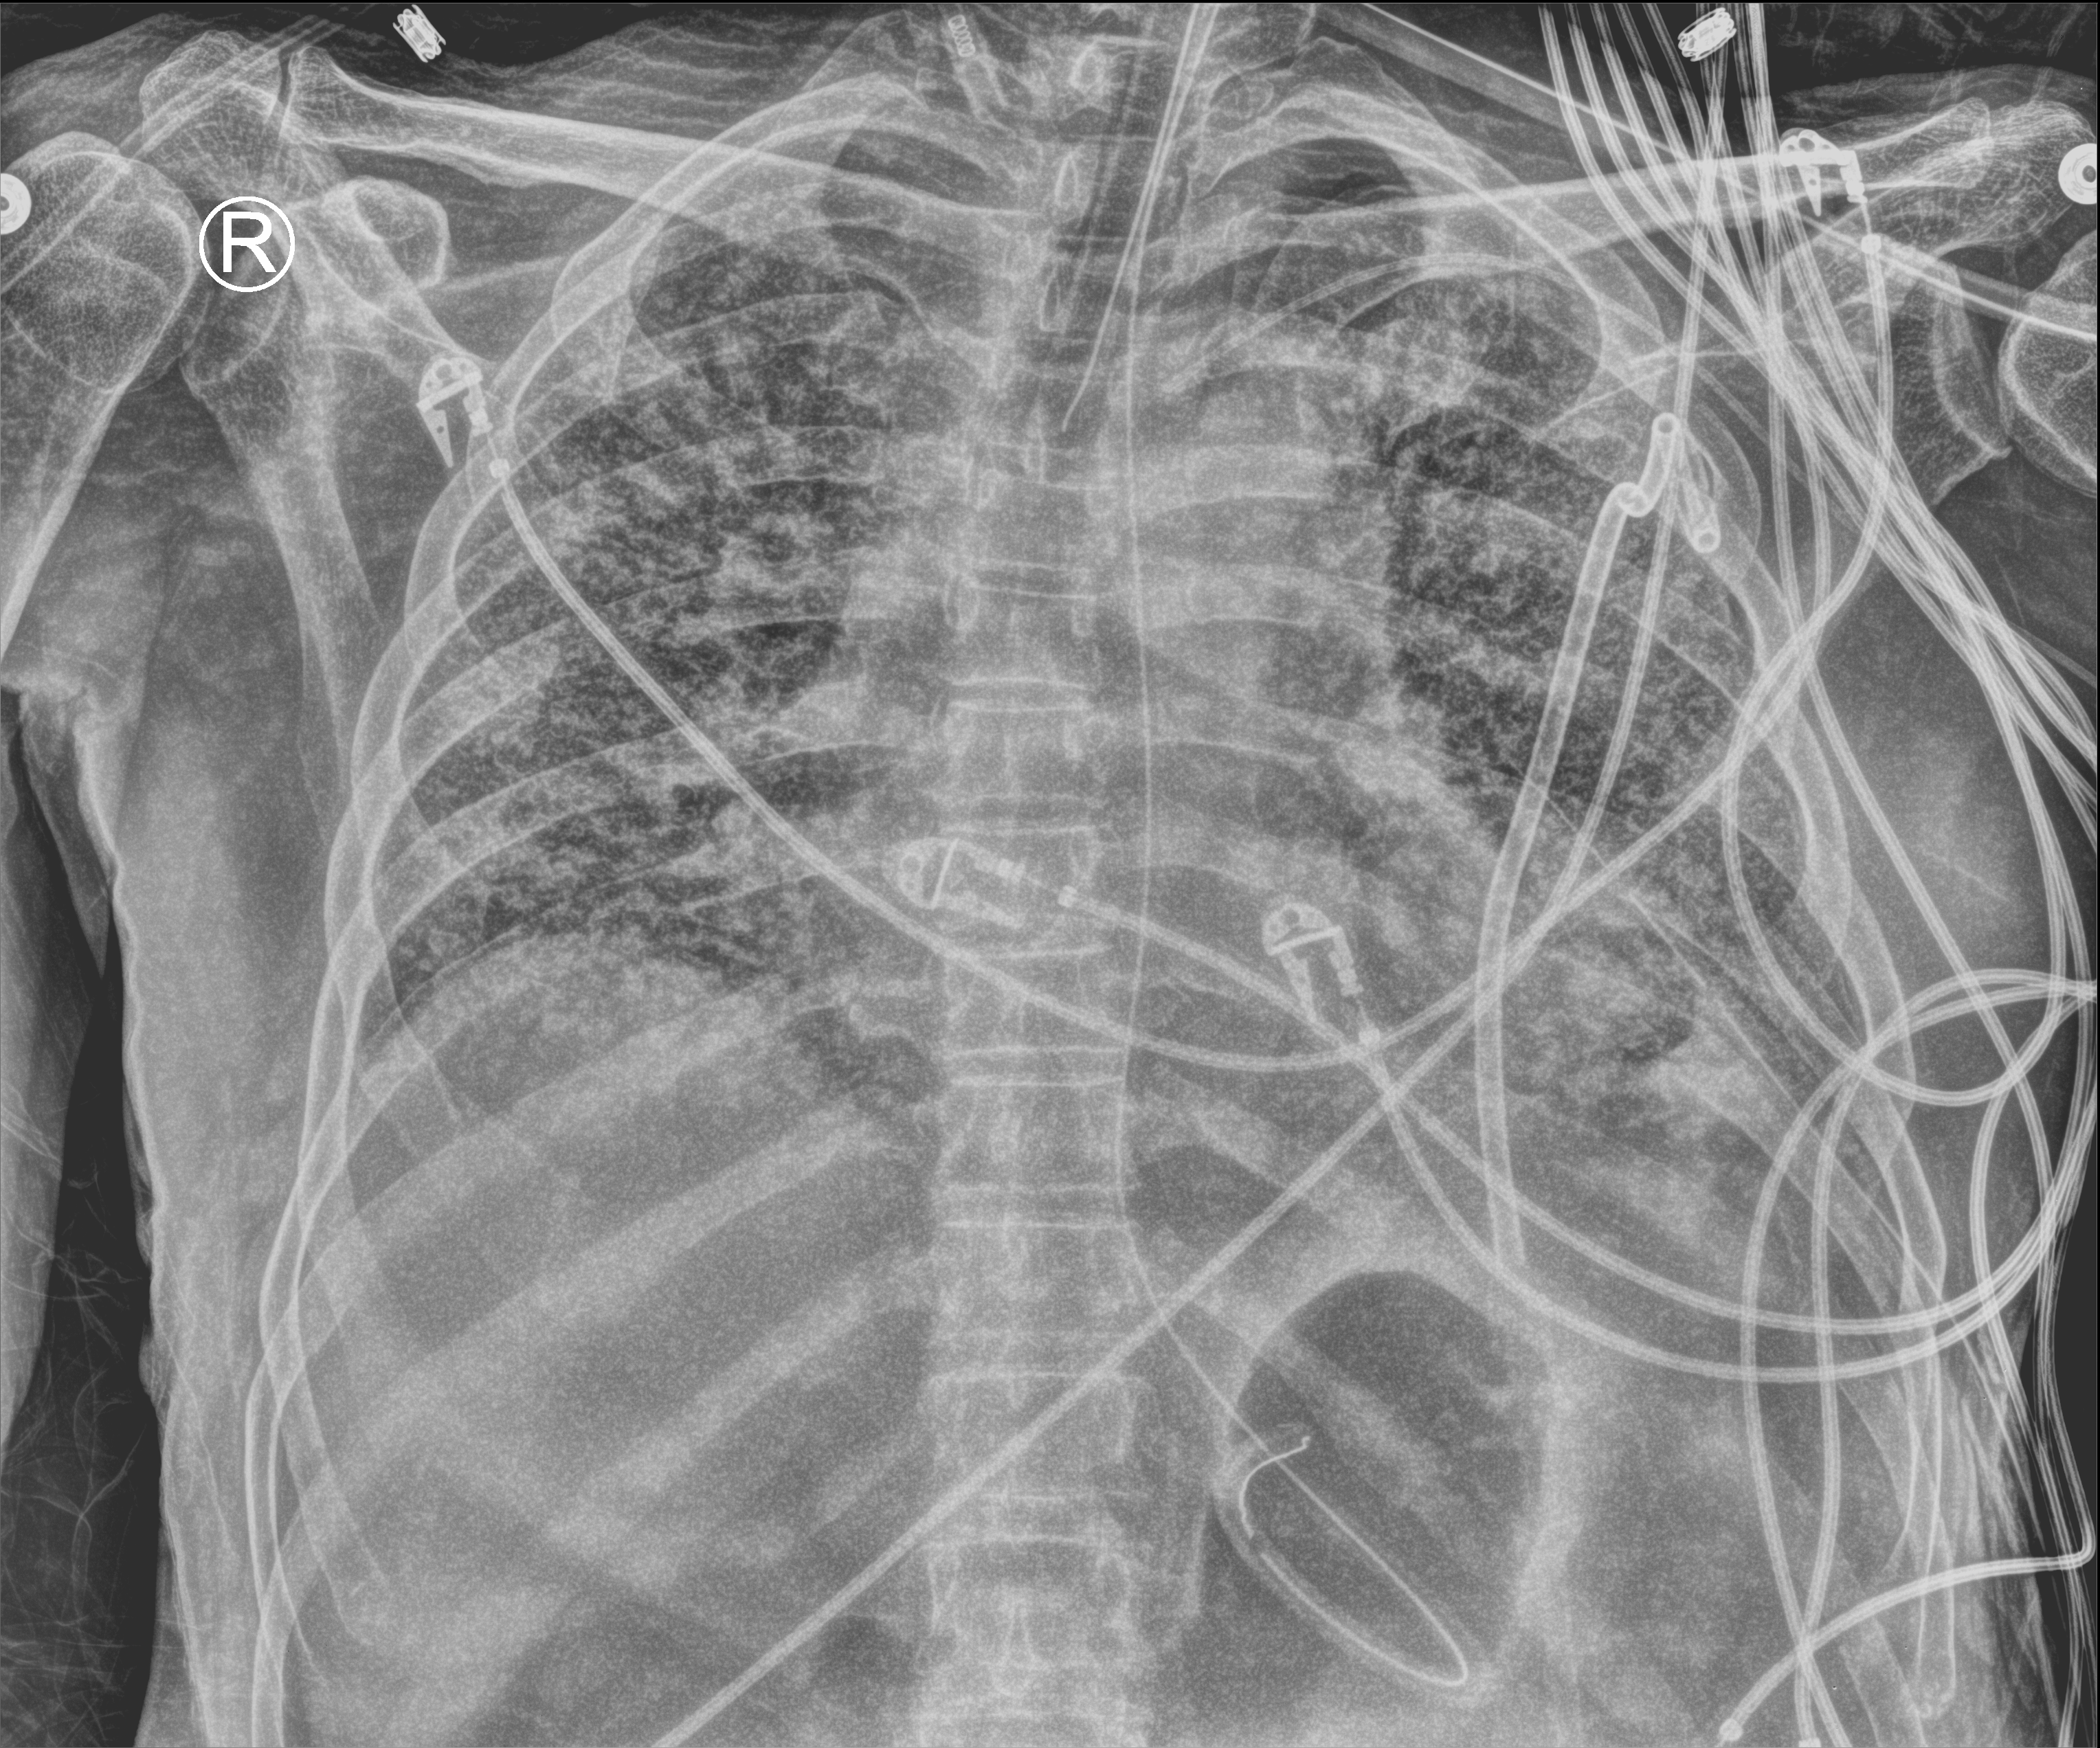
Portable chest radiograph; anteroposterior (AP) projection. Male patient hospitalised with COVID-19, age 60–74 years.
Hospital-stay facts (about this admission, not read from this image; timing relative to this image not recorded): admitted to intensive care during this hospital stay: yes.